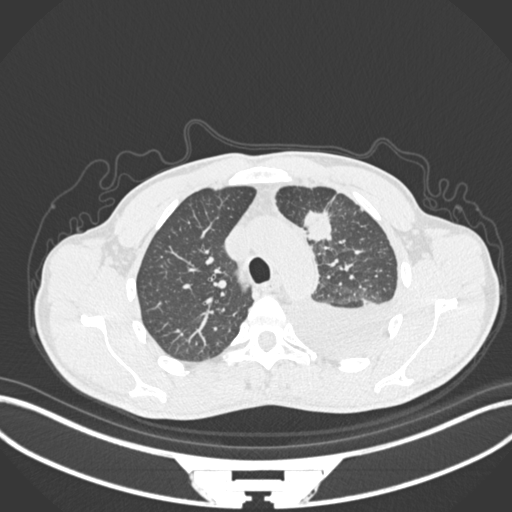
Chest CT, one axial slice. Position 164 of 244 along the scan axis. Lung window (W 1500 / L -600 HU). 1 mm slice thickness. 512 × 512 image matrix, field of view 400 × 400 mm. Patient: male, 49 years. From the clinical record (not read from this slice): clinical TNM (as recorded): T1c N1 M1.
Annotated regions visible in this slice (bounding box drawn by a radiologist):
- lung tumour (recorded histology: adenocarcinoma): bounding box (x1, y1, x2, y2) in pixels: (303, 203, 336, 242)